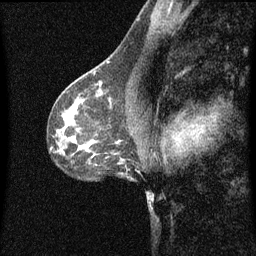
Breast MRI (dynamic contrast-enhanced), one sagittal slice; slice 40 of 60 in the series (ordered by position); dynamic contrast-enhanced series, image 2 of 3 at this slice position (ordered by acquisition); 1.5 T; TE 4.2 ms, TR 8.4 ms; 2 mm slice thickness; 256 × 256 image matrix, field of view 200 × 200 mm. Patient: female, 41 years.
Annotated regions visible in this slice (semi-automatic segmentation, software-assisted and operator-edited):
- analysis volume of interest (the breast-tissue region the enhancement analysis was run in; not a lesion): bounding box <94,72,119,97> (left, top, right, bottom; pixels)
- tumour enhancement mask (voxels above the 70 % enhancement threshold inside the analysis volume of interest): <94,72,101,85>